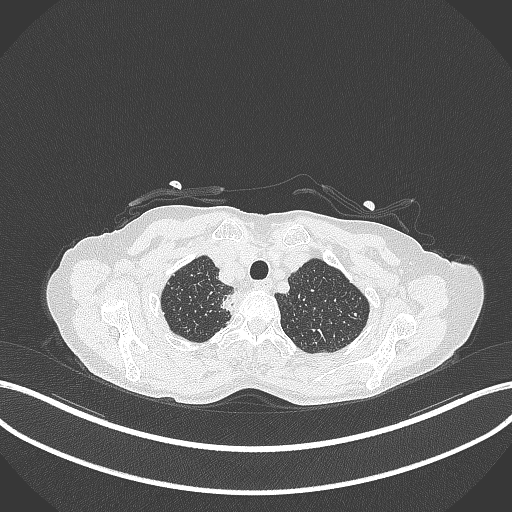
Chest CT, one axial slice; lung window (W 1500 / L -600 HU); 1 mm slice thickness; 512 × 512 image matrix. Patient: female, 75 years. Case-level facts recorded for this patient, not image findings: clinical TNM (as recorded): T1c N1 M1.
Annotated regions visible in this slice (rectangle marked by the reading radiologist):
- lung tumour (recorded histology: adenocarcinoma): bounding box <219,289,240,314> (left, top, right, bottom; pixels)